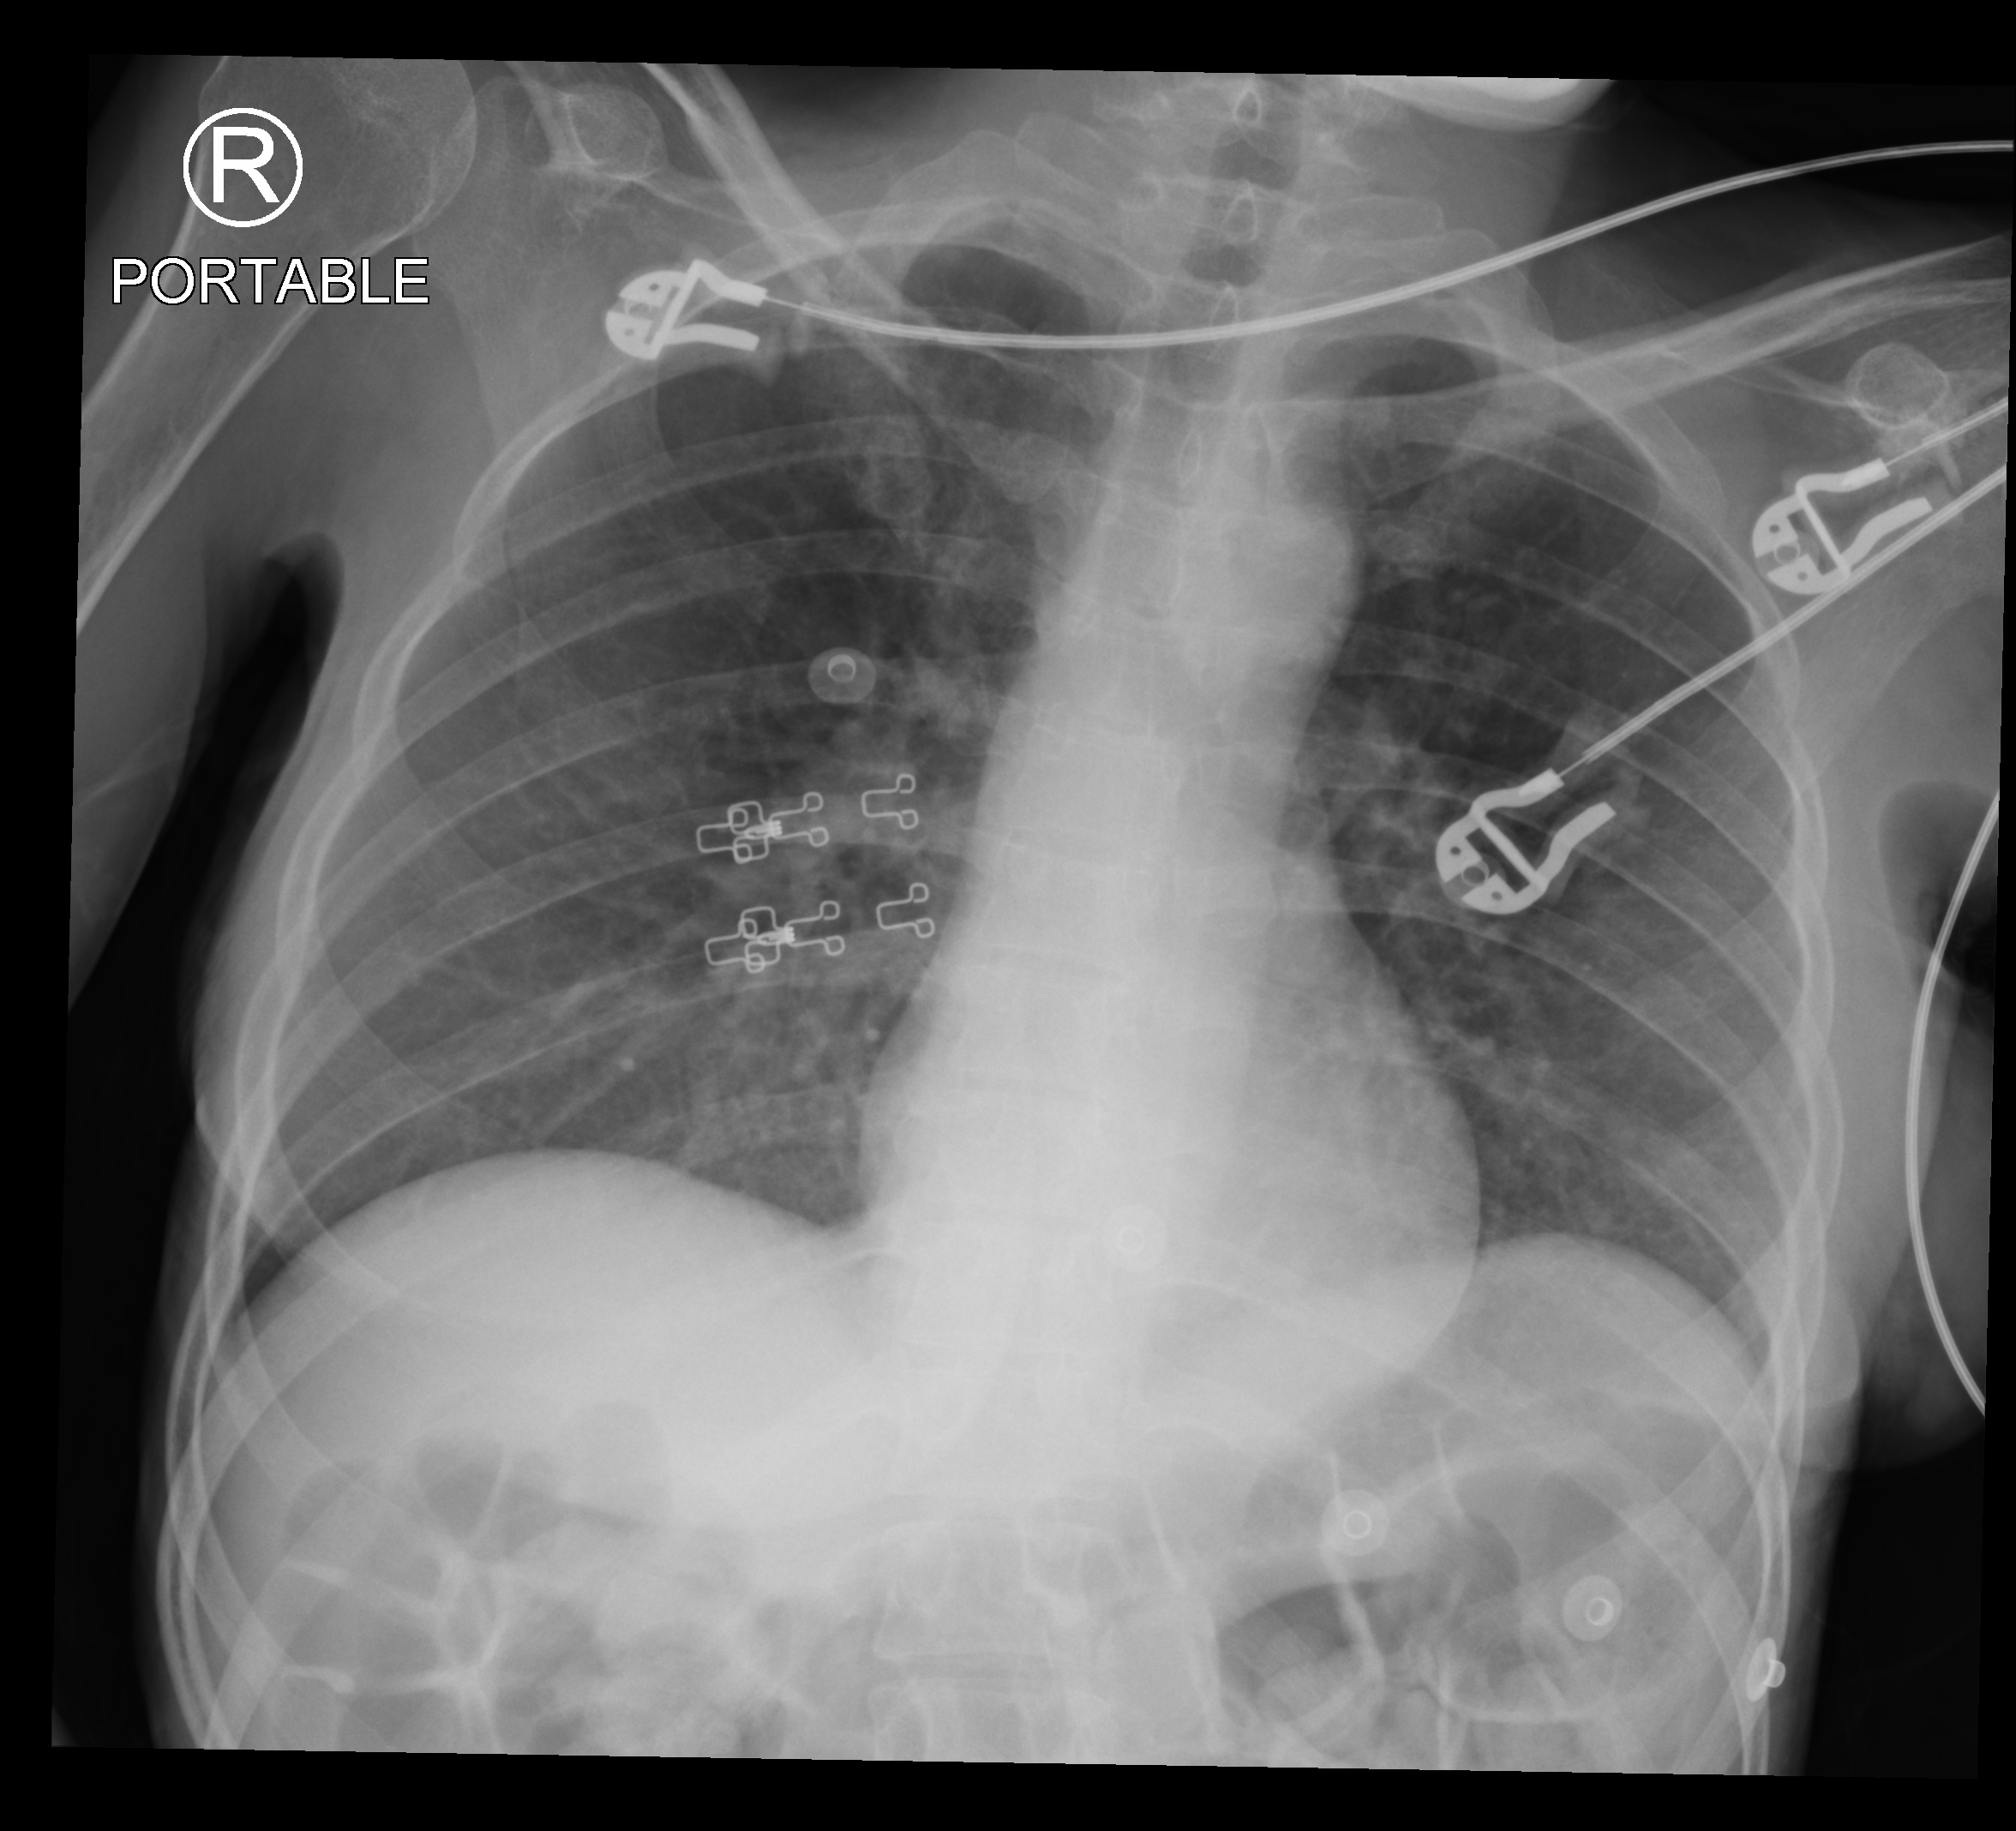
Chest X-ray (portable), anteroposterior (AP) projection. Female patient hospitalised with COVID-19, age 18–59 years.
Admission-level facts for this patient (not findings on this image; timing relative to this image not recorded):
- COPD (admission record): no
- length of hospital stay: 4 days
- mechanically ventilated during this hospital stay: no